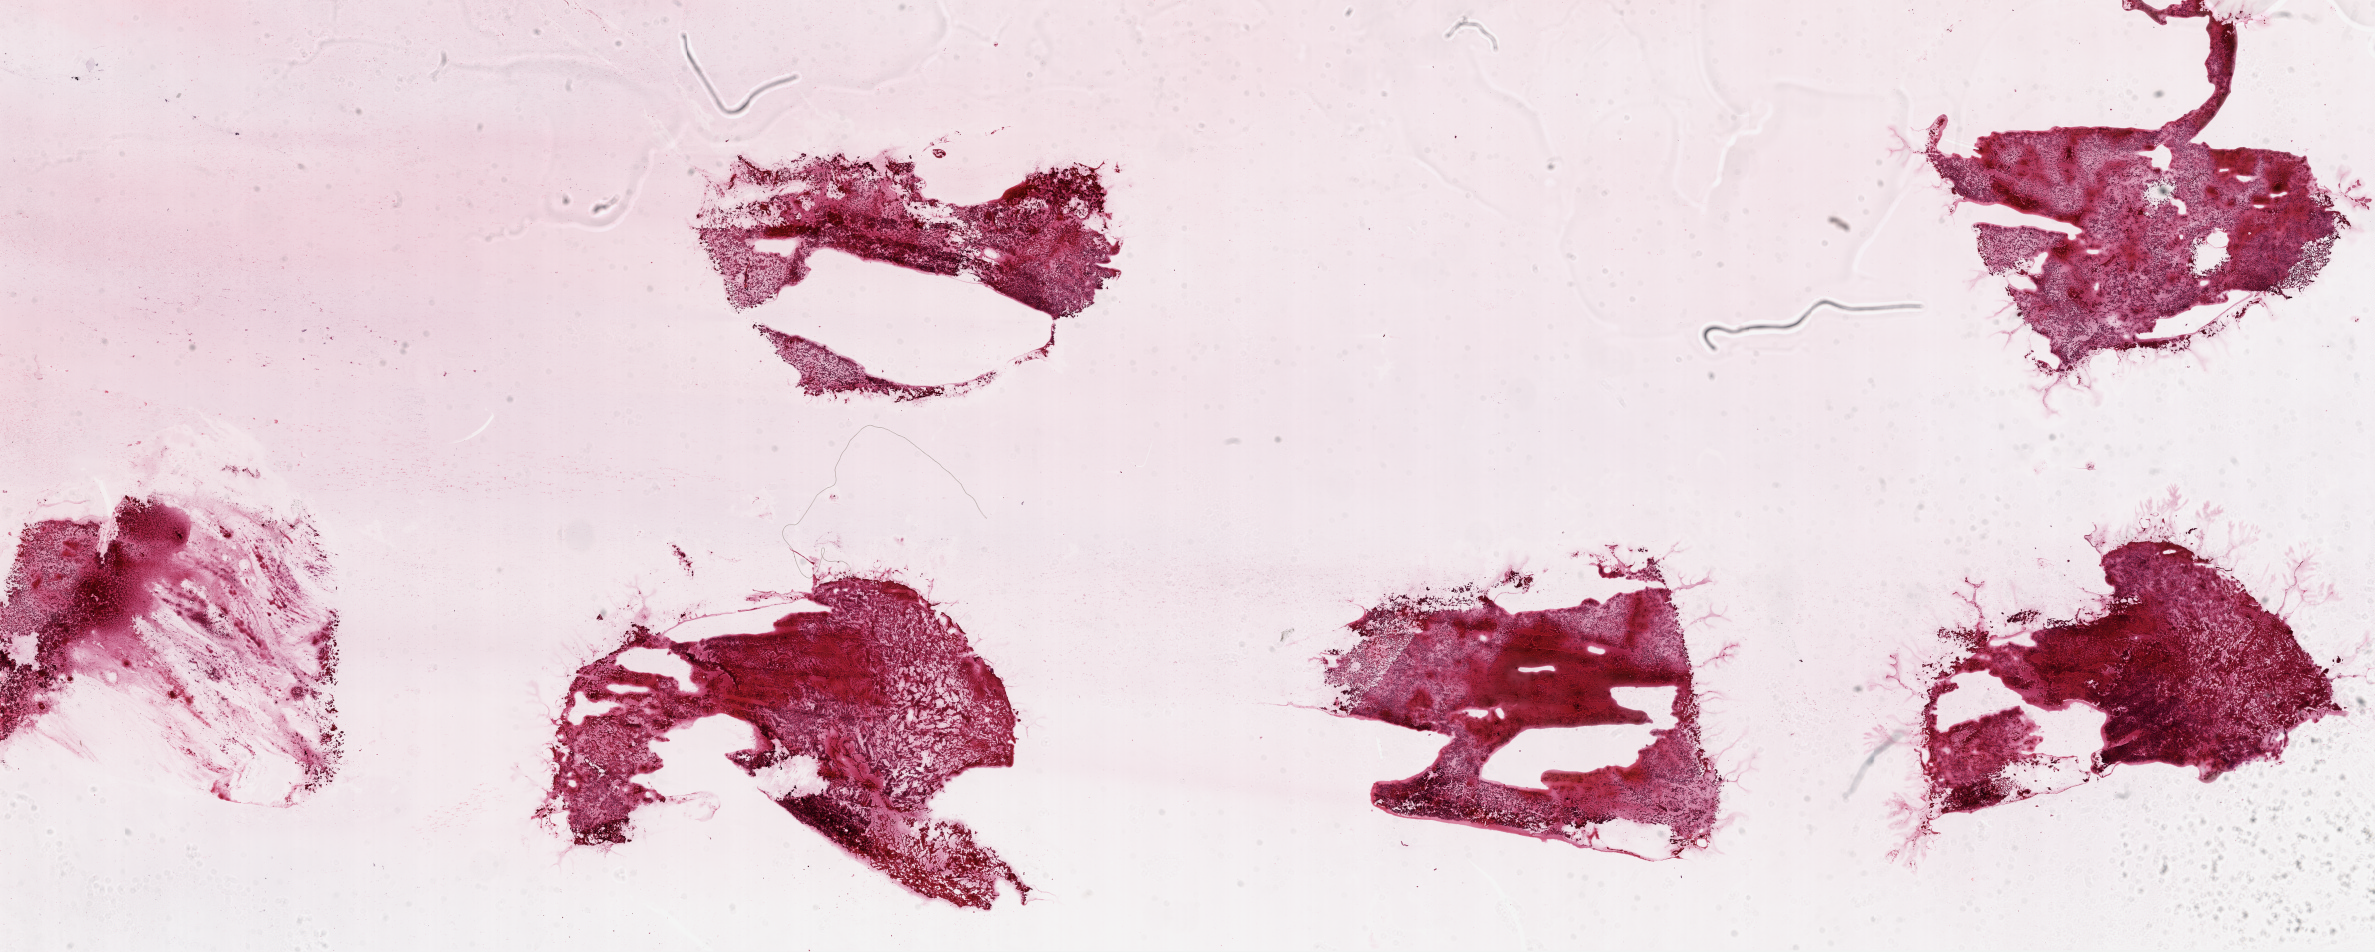
Digitized H&E-stained tissue section (whole slide), a low-resolution overview of the entire scanned area, about 38.1 x 15.3 mm (from a 20x scan). Frozen section from the top of the tissue portion. Sample: primary tumour, brain. Male patient; age at initial diagnosis 76 years. Pathologist review of this section (percent, as recorded): tumour cells 100%, tumour nuclei 80%, normal cells 0%, stromal cells 0%, necrosis 0%.
Pathologic diagnosis: Glioblastoma.